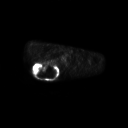
FDG PET of an extremity soft-tissue mass (from a PET/CT study), one axial slice. Slice 203 of 267 in the series (ordered by position). 3.27 mm slice thickness. 128 × 128 image matrix. Patient: male, 61 years. From the clinical record (not read from this slice): histological type: pleiomorphic spindle cell undifferentiated; grade: high; site of the primary tumour: right parascapusular.
Annotated regions visible in this slice (expert contour drawn on MRI and transferred to this co-registered scan by the dataset authors):
- gross tumour volume including surrounding oedema: bounding box (x1, y1, x2, y2) in pixels: (32, 61, 60, 78)
- gross tumour volume (mass): (32, 62, 58, 77)